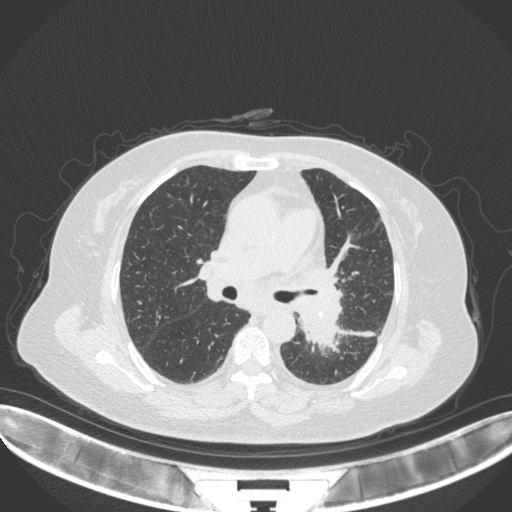
Chest CT, one axial slice; slice 204 of 328 in the series (ordered by position); lung window (W 1500 / L -600 HU); 512 × 512 image matrix, field of view 400 × 400 mm. Patient: female, 69 years. From the clinical record (not read from this slice): clinical TNM (as recorded): T2b N3 M1.
Outlined on this slice (rectangle marked by the reading radiologist):
- lung tumour (recorded histology: adenocarcinoma): bounding box [x1, y1, x2, y2] px = [296, 298, 346, 352]